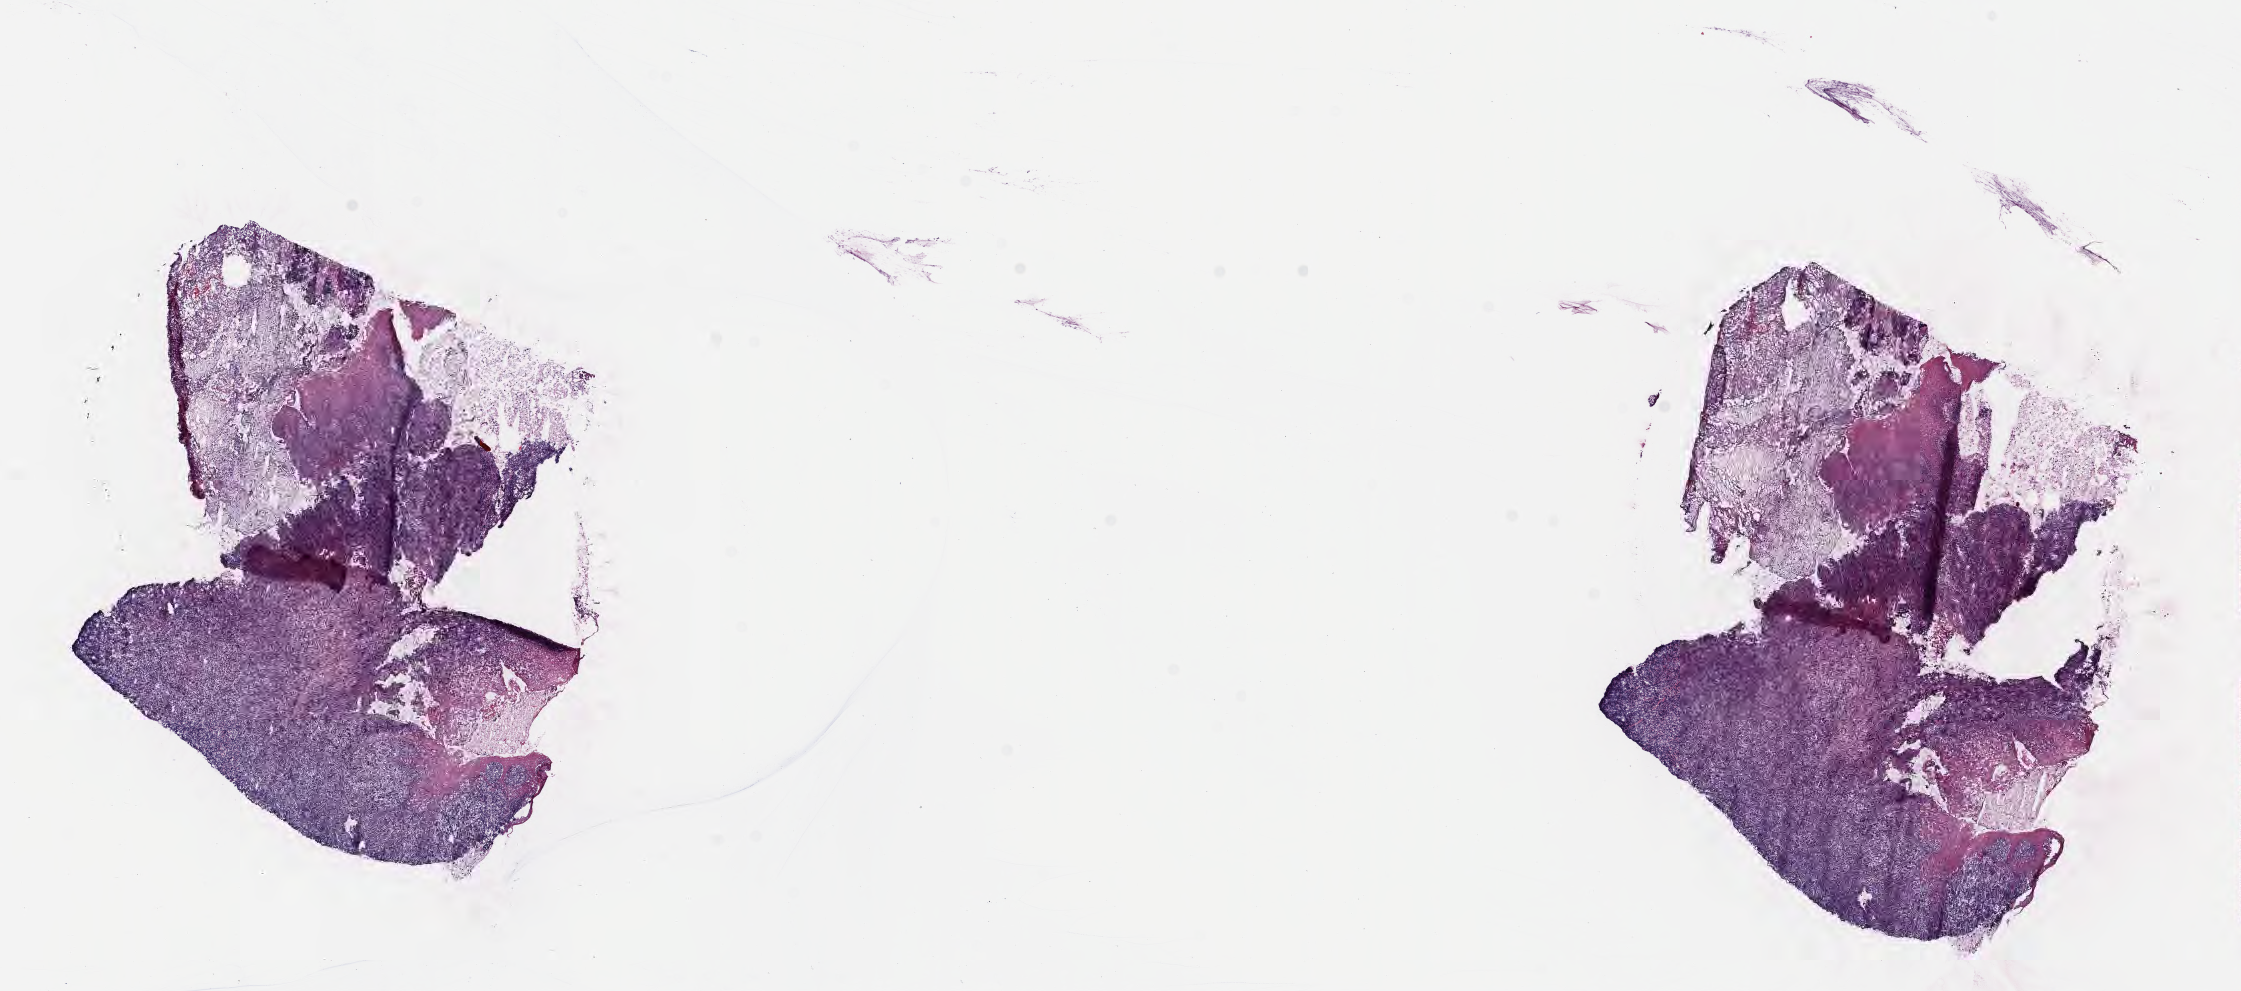
Digitized H&E-stained section, whole scanned area (about 18.1 x 8.0 mm) shown as a low-resolution overview; frozen section (tissue freezing medium); primary tumor; anatomic site: cranium. Male patient, age 11 years. Pathologist review of this section (percent, as recorded): tumor cells 50%, tumor nuclei 70%, stromal cells 20%, necrosis 10%, normal cells 20%. Inflammatory infiltration, as recorded: lymphocyte infiltration 40%, monocyte infiltration 20%, neutrophil infiltration 0%.
Histologic diagnosis: Diffuse large B-cell lymphoma, NOS. Ann Arbor stage (patient): Stage III.